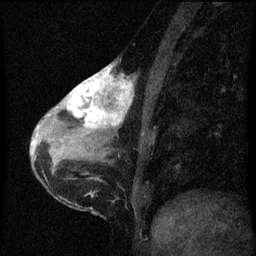
Breast MRI (dynamic contrast-enhanced), one sagittal slice; position 21 of 60 along the scan axis; dynamic contrast-enhanced series, image 2 of 3 at this slice position (ordered by acquisition); 1.5 T; TE 4.2 ms, TR 8 ms; 2 mm slice thickness; 256 × 256 image matrix. Female patient, age 38 years.
Outlined on this slice (semi-automatically segmented with operator editing):
- analysis volume of interest (the breast-tissue region the enhancement analysis was run in; not a lesion): bounding box <61,64,136,147> (left, top, right, bottom; pixels)
- tumour enhancement mask (voxels above the 70 % enhancement threshold inside the analysis volume of interest): <63,64,134,129>